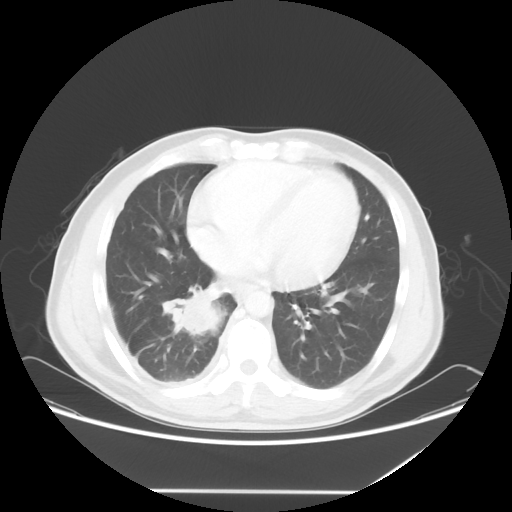
Chest CT, one axial slice. Reconstruction kernel STANDARD. 120 kVp. Lung window (W 1500 / L -600 HU). 5 mm slice thickness. 512 × 512 image matrix. Male patient, age 48 years. From the clinical record (not read from this slice): clinical TNM (as recorded): T3 N3 M1a.
Outlined on this slice (rectangle marked by the reading radiologist):
- lung tumour (recorded histology: squamous cell carcinoma): bounding box [x1, y1, x2, y2] px = [157, 285, 232, 342]